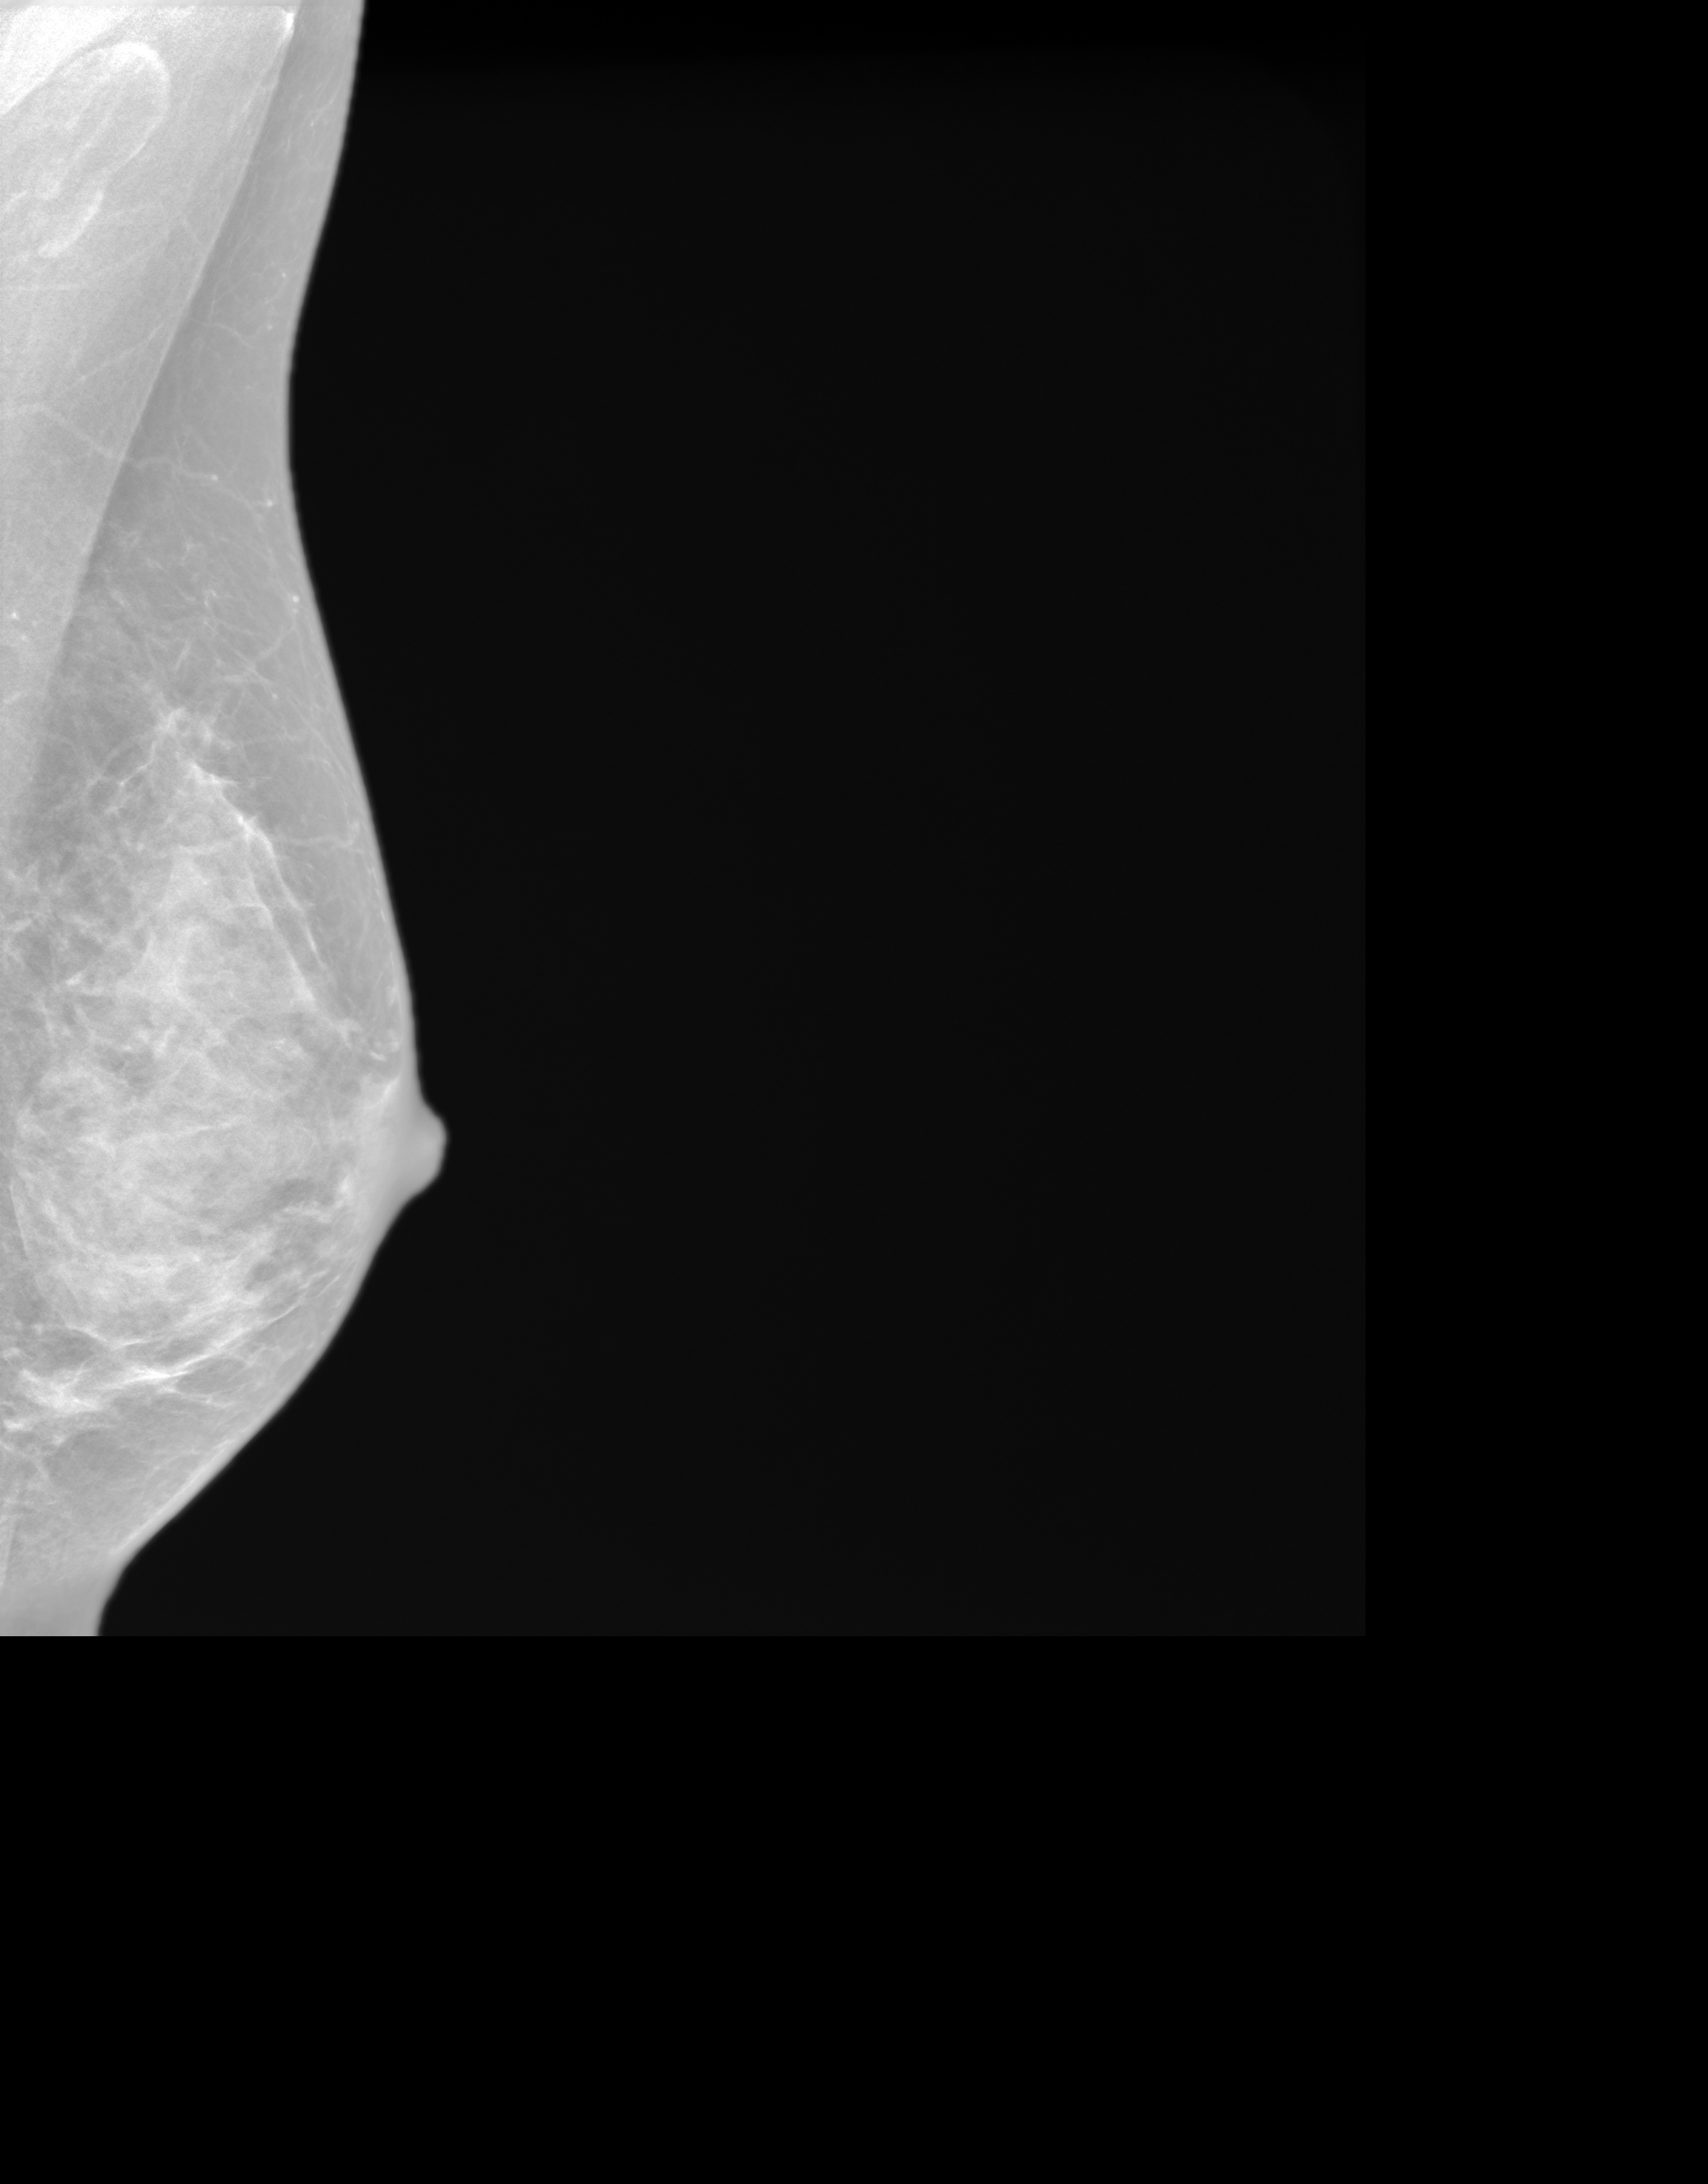
Synthetic 2-D view generated from a tomosynthesis acquisition (not an FFDM exposure); left breast; MLO view; annual screening mammography examination. Female patient, age 55 years.
Breast density at the screening exam (both breasts): extremely dense (BI-RADS density category d). Final BI-RADS category for the screening round (tomosynthesis exam, both breasts): category 1. Recall: no recall after this screen.